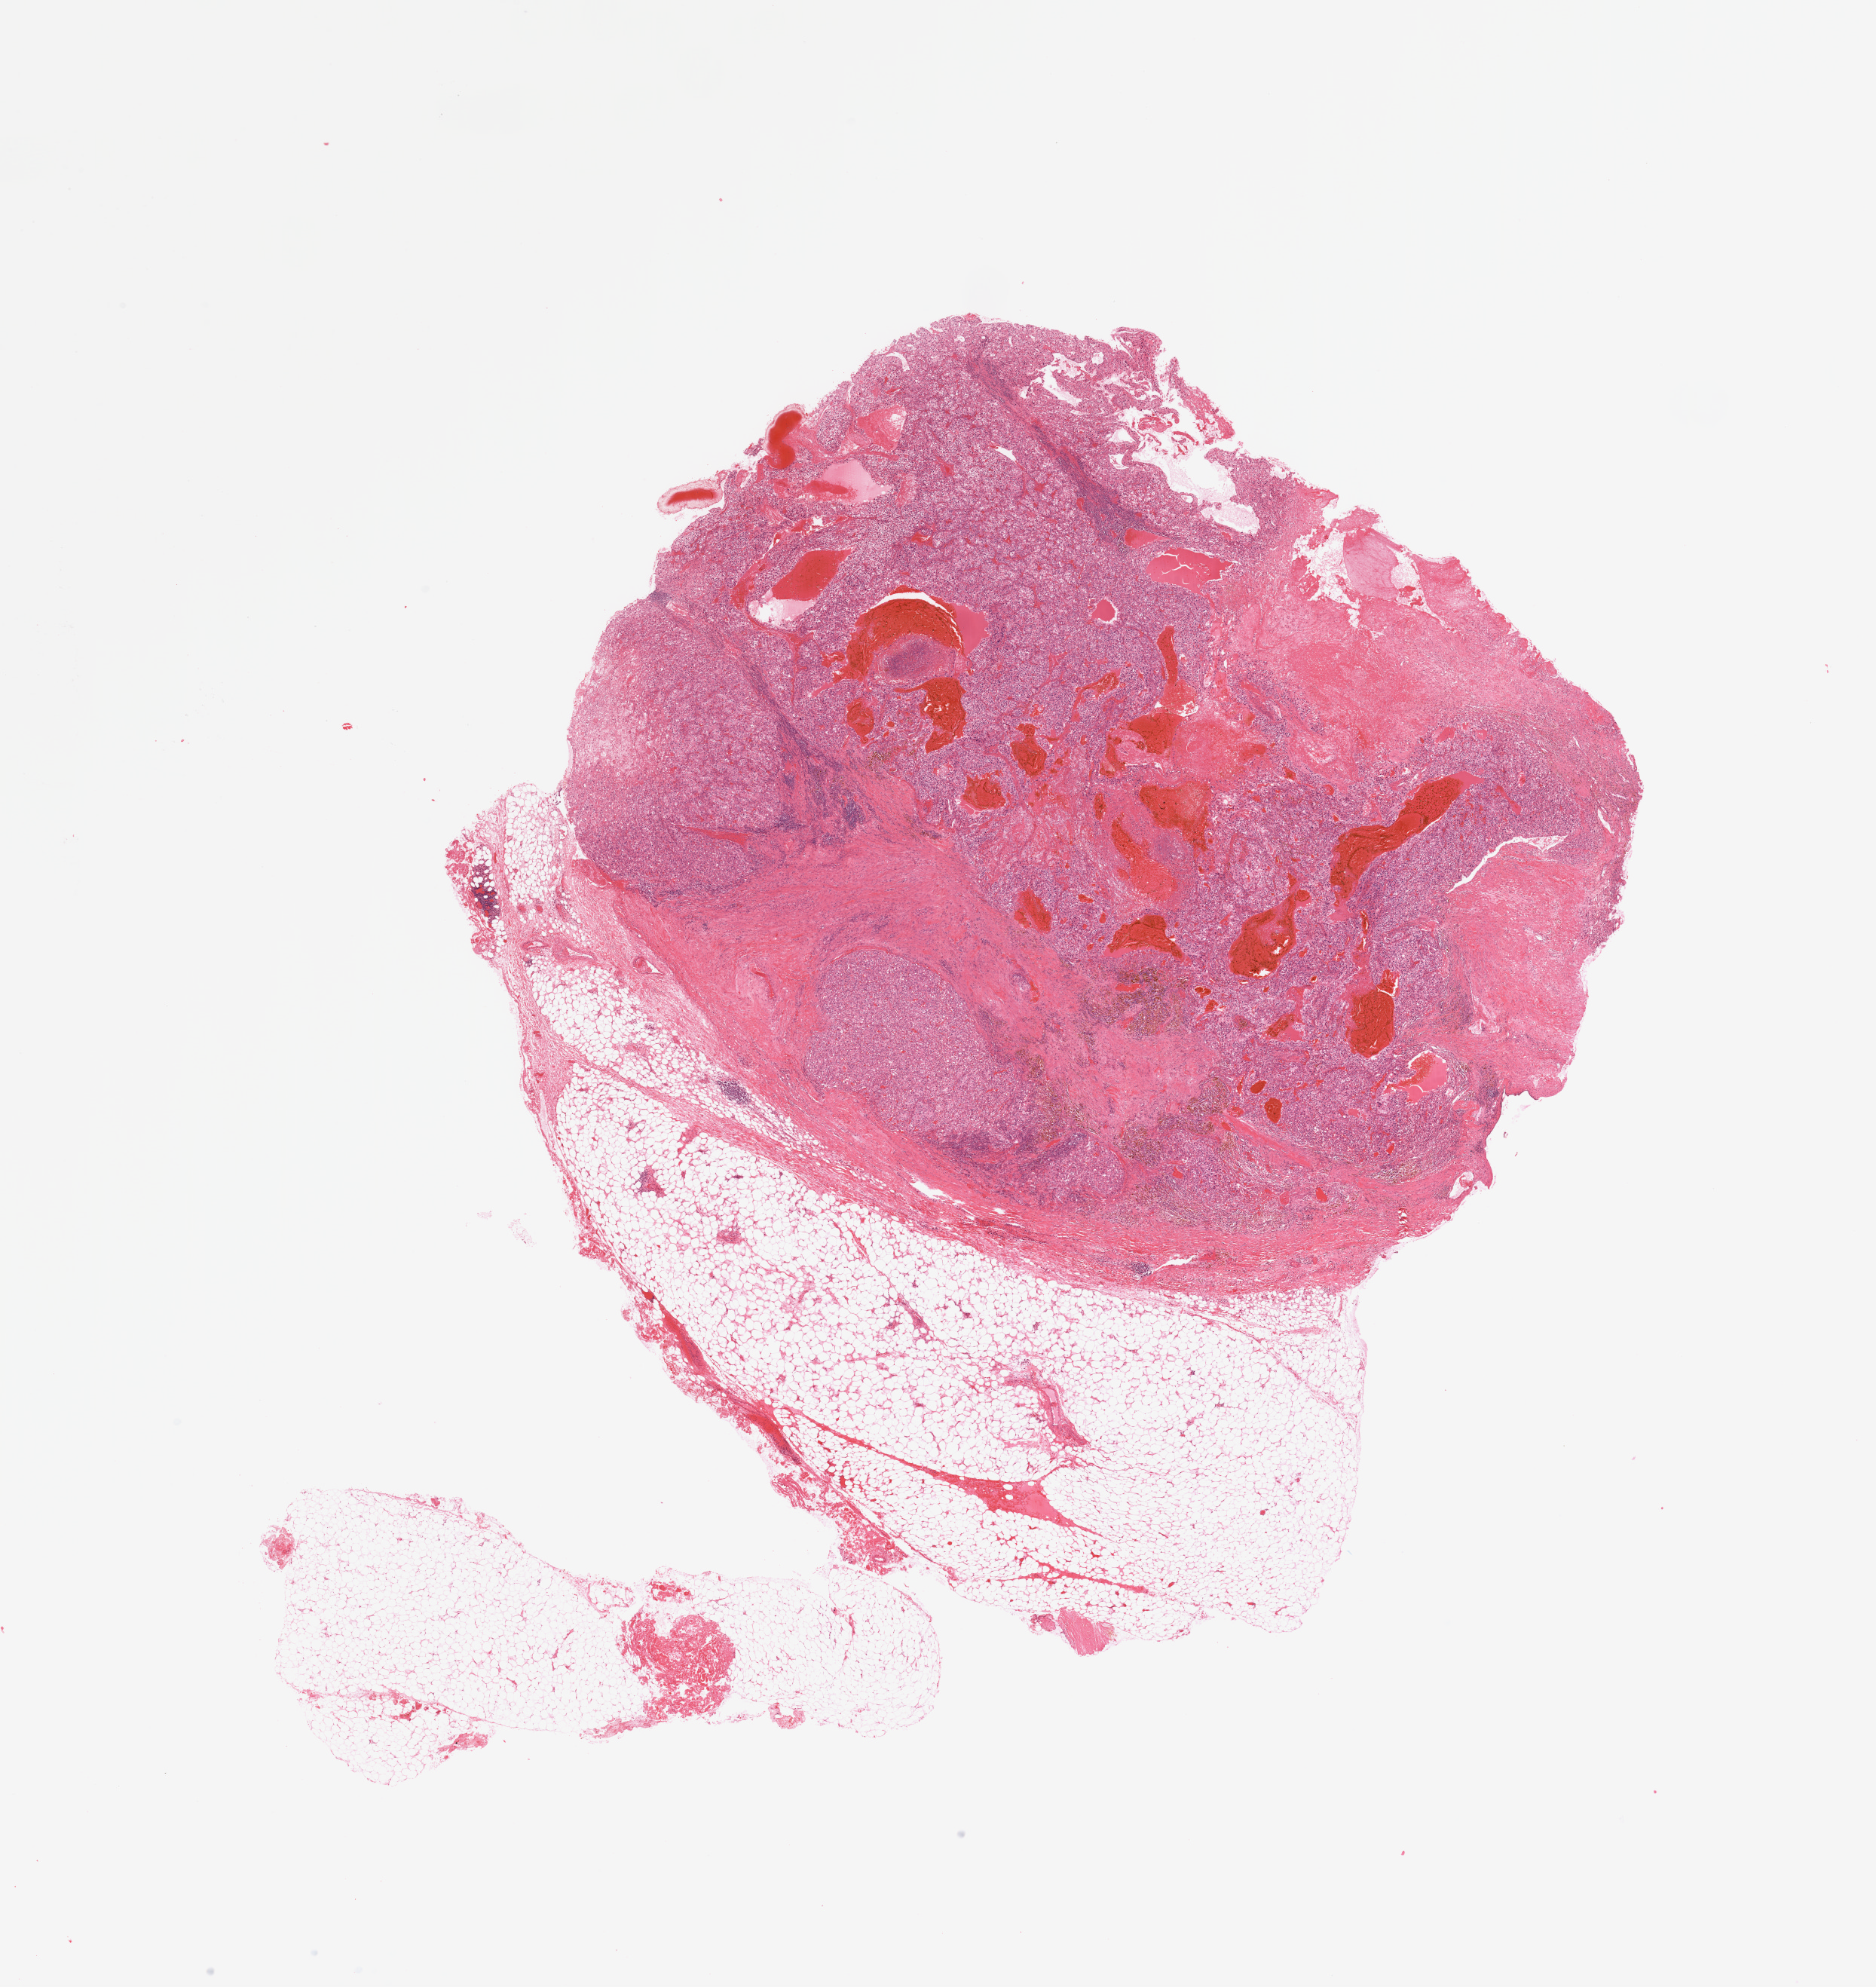
Hematoxylin and eosin (H&E) stained whole-slide image, shown as a low-resolution overview of the whole scanned area (about 19.7 x 20.9 mm); tumour tissue sample, sampled site: kidney. Male, 72 y/o. Histologic grade: G3 (poorly differentiated). Slide review estimates, as recorded: tumour nuclei 80%, necrosis 20%.
Diagnosis: Renal cell carcinoma, NOS. AJCC pathologic stage: IV.